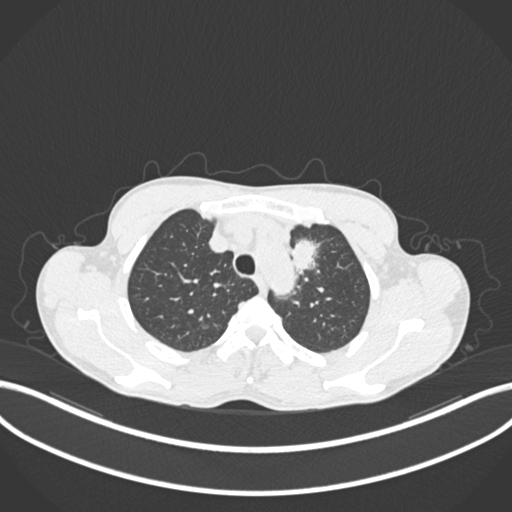
Chest CT, one axial slice. Position 164 of 211 along the scan axis. Reconstruction kernel B30f. 120 kVp. Lung window (W 1500 / L -600 HU). 512 × 512 image matrix, field of view 400 × 400 mm. Patient: male, 58 years. From the clinical record (not read from this slice): clinical TNM (as recorded): T1c N1 M0.
Outlined on this slice (rectangle marked by the reading radiologist):
- lung tumour (recorded histology: adenocarcinoma): box from (x=285, y=236) to (x=322, y=280) px